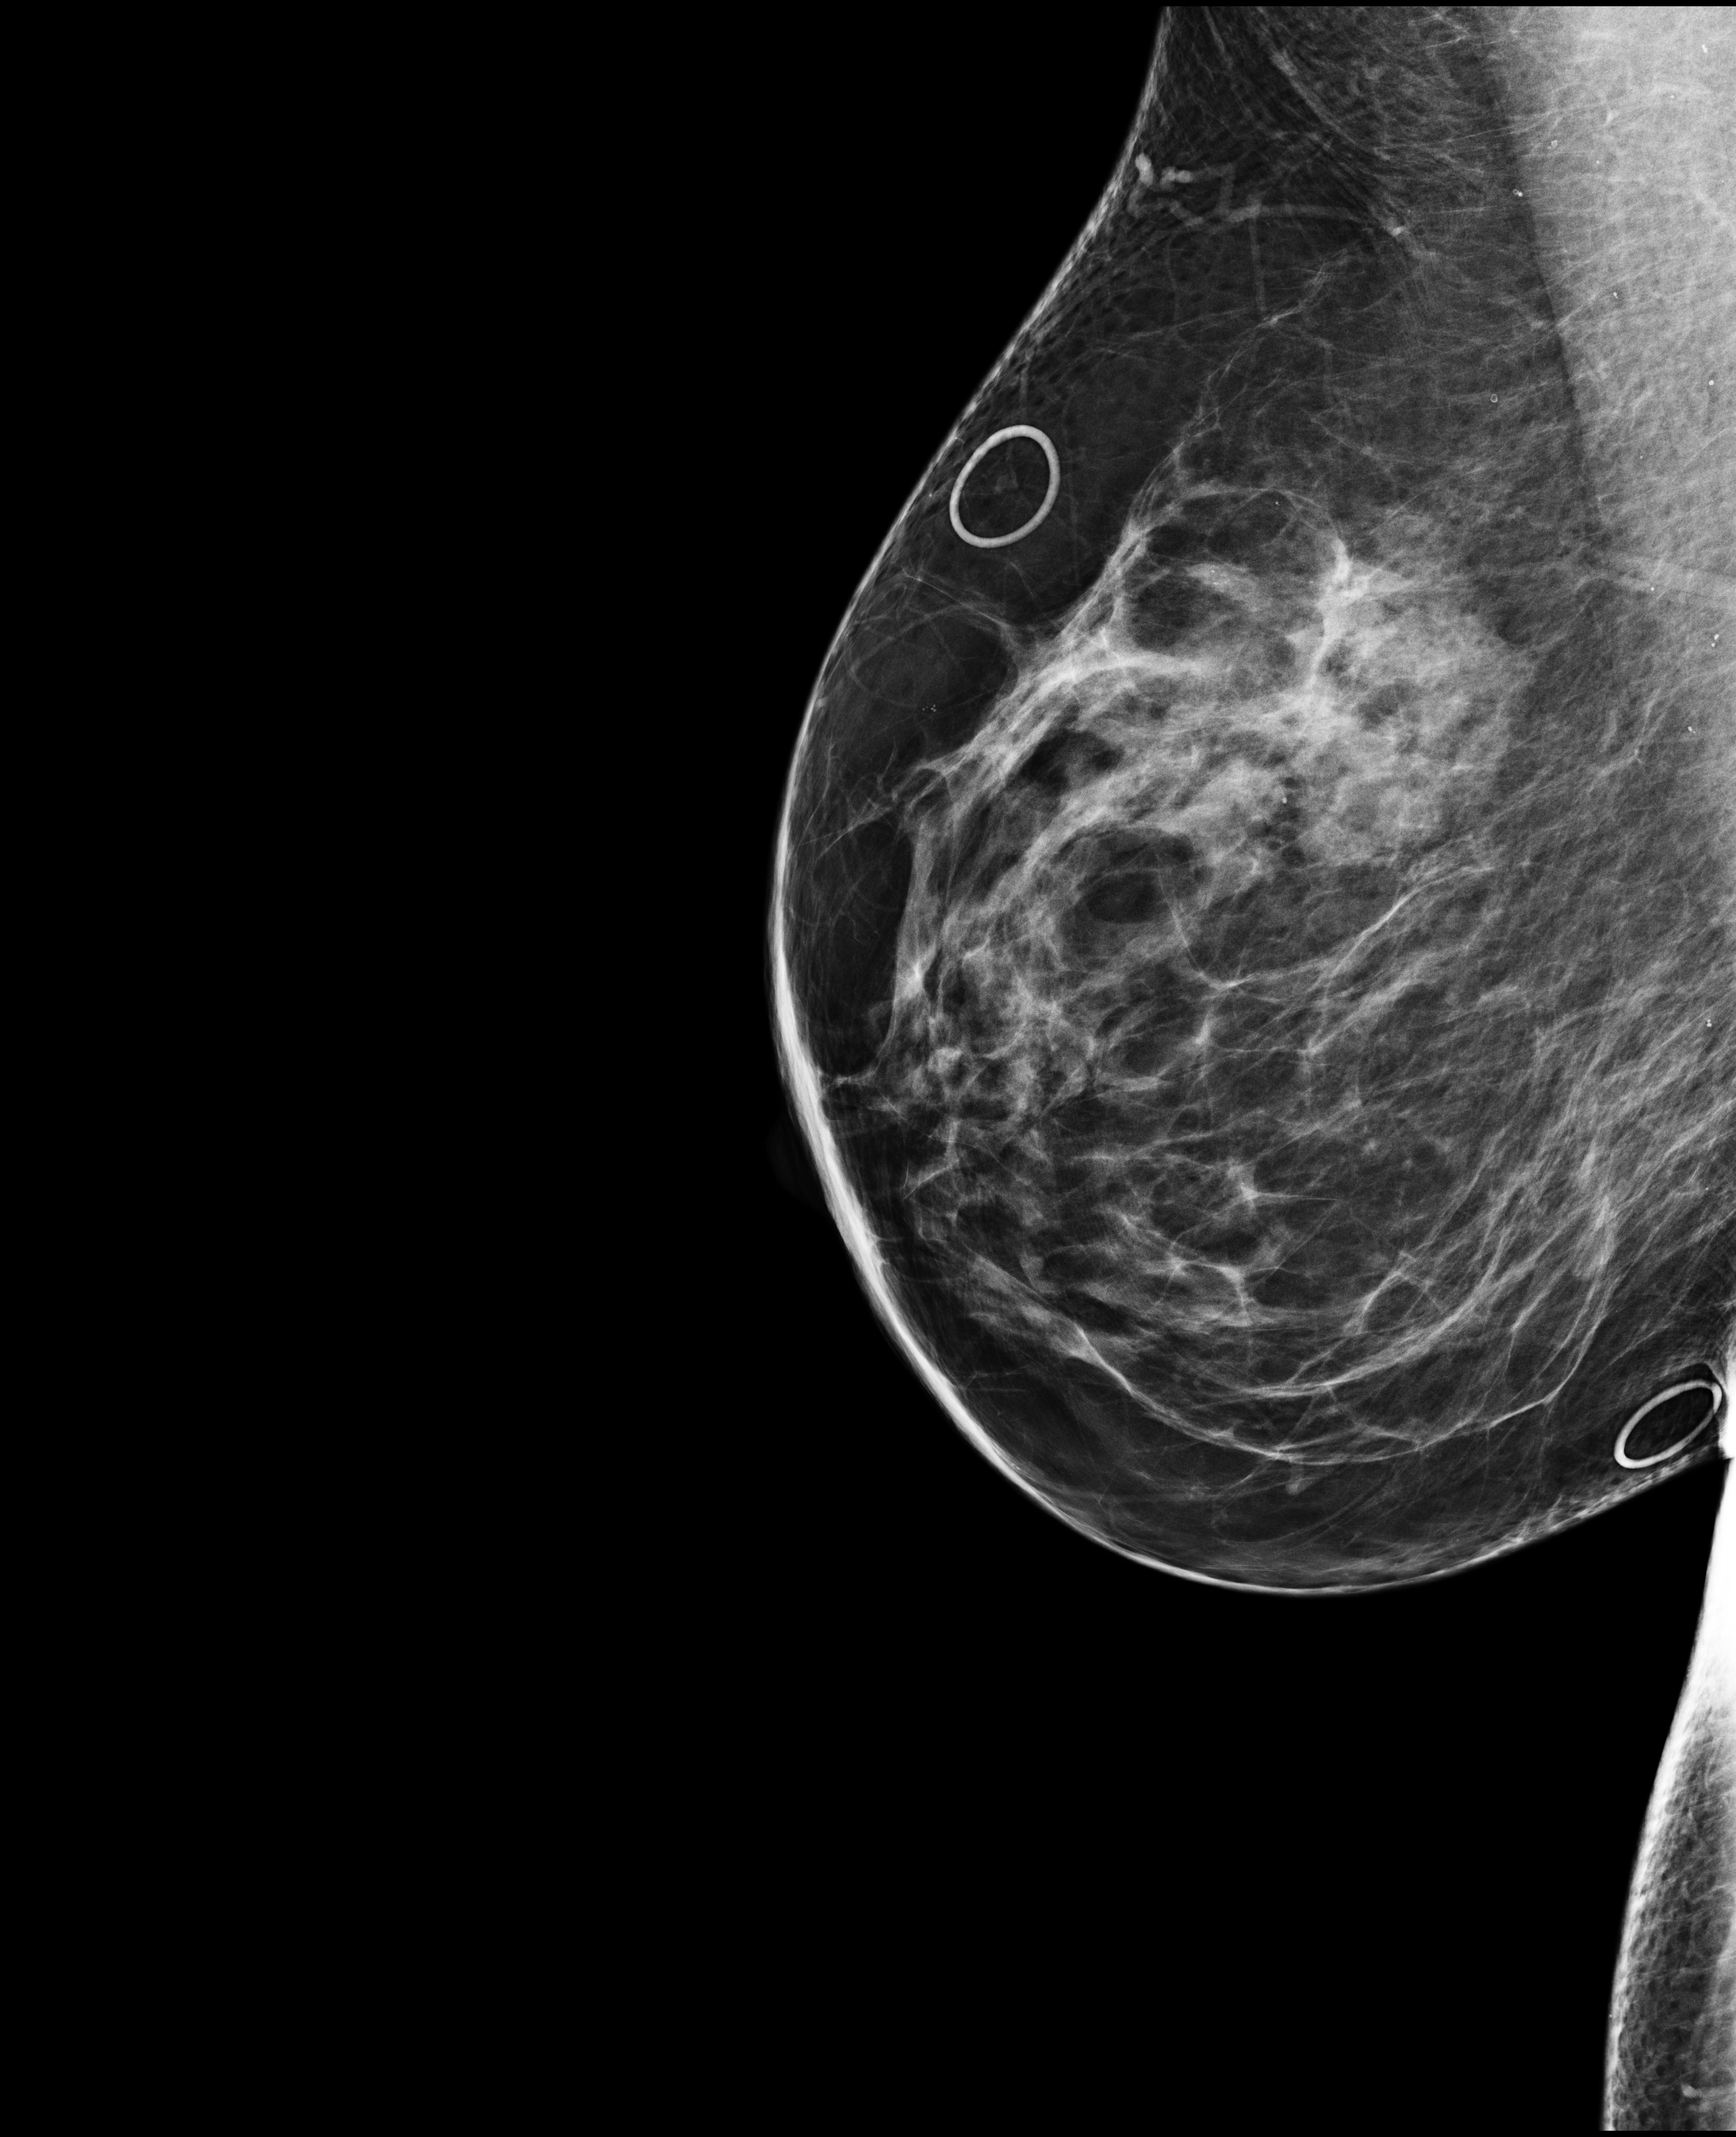
Full-field digital mammogram (FFDM), right breast, mediolateral (ML) view, diagnostic examination (additional views), compressed breast thickness 74 mm. Patient: female, 60 years.
BI-RADS breast density category at the screening exam (both breasts, scale 1–4): 3. Final BI-RADS assessment for this screening round (tomosynthesis exam, both breasts): category 1. Recall: recalled for additional imaging after this screen.